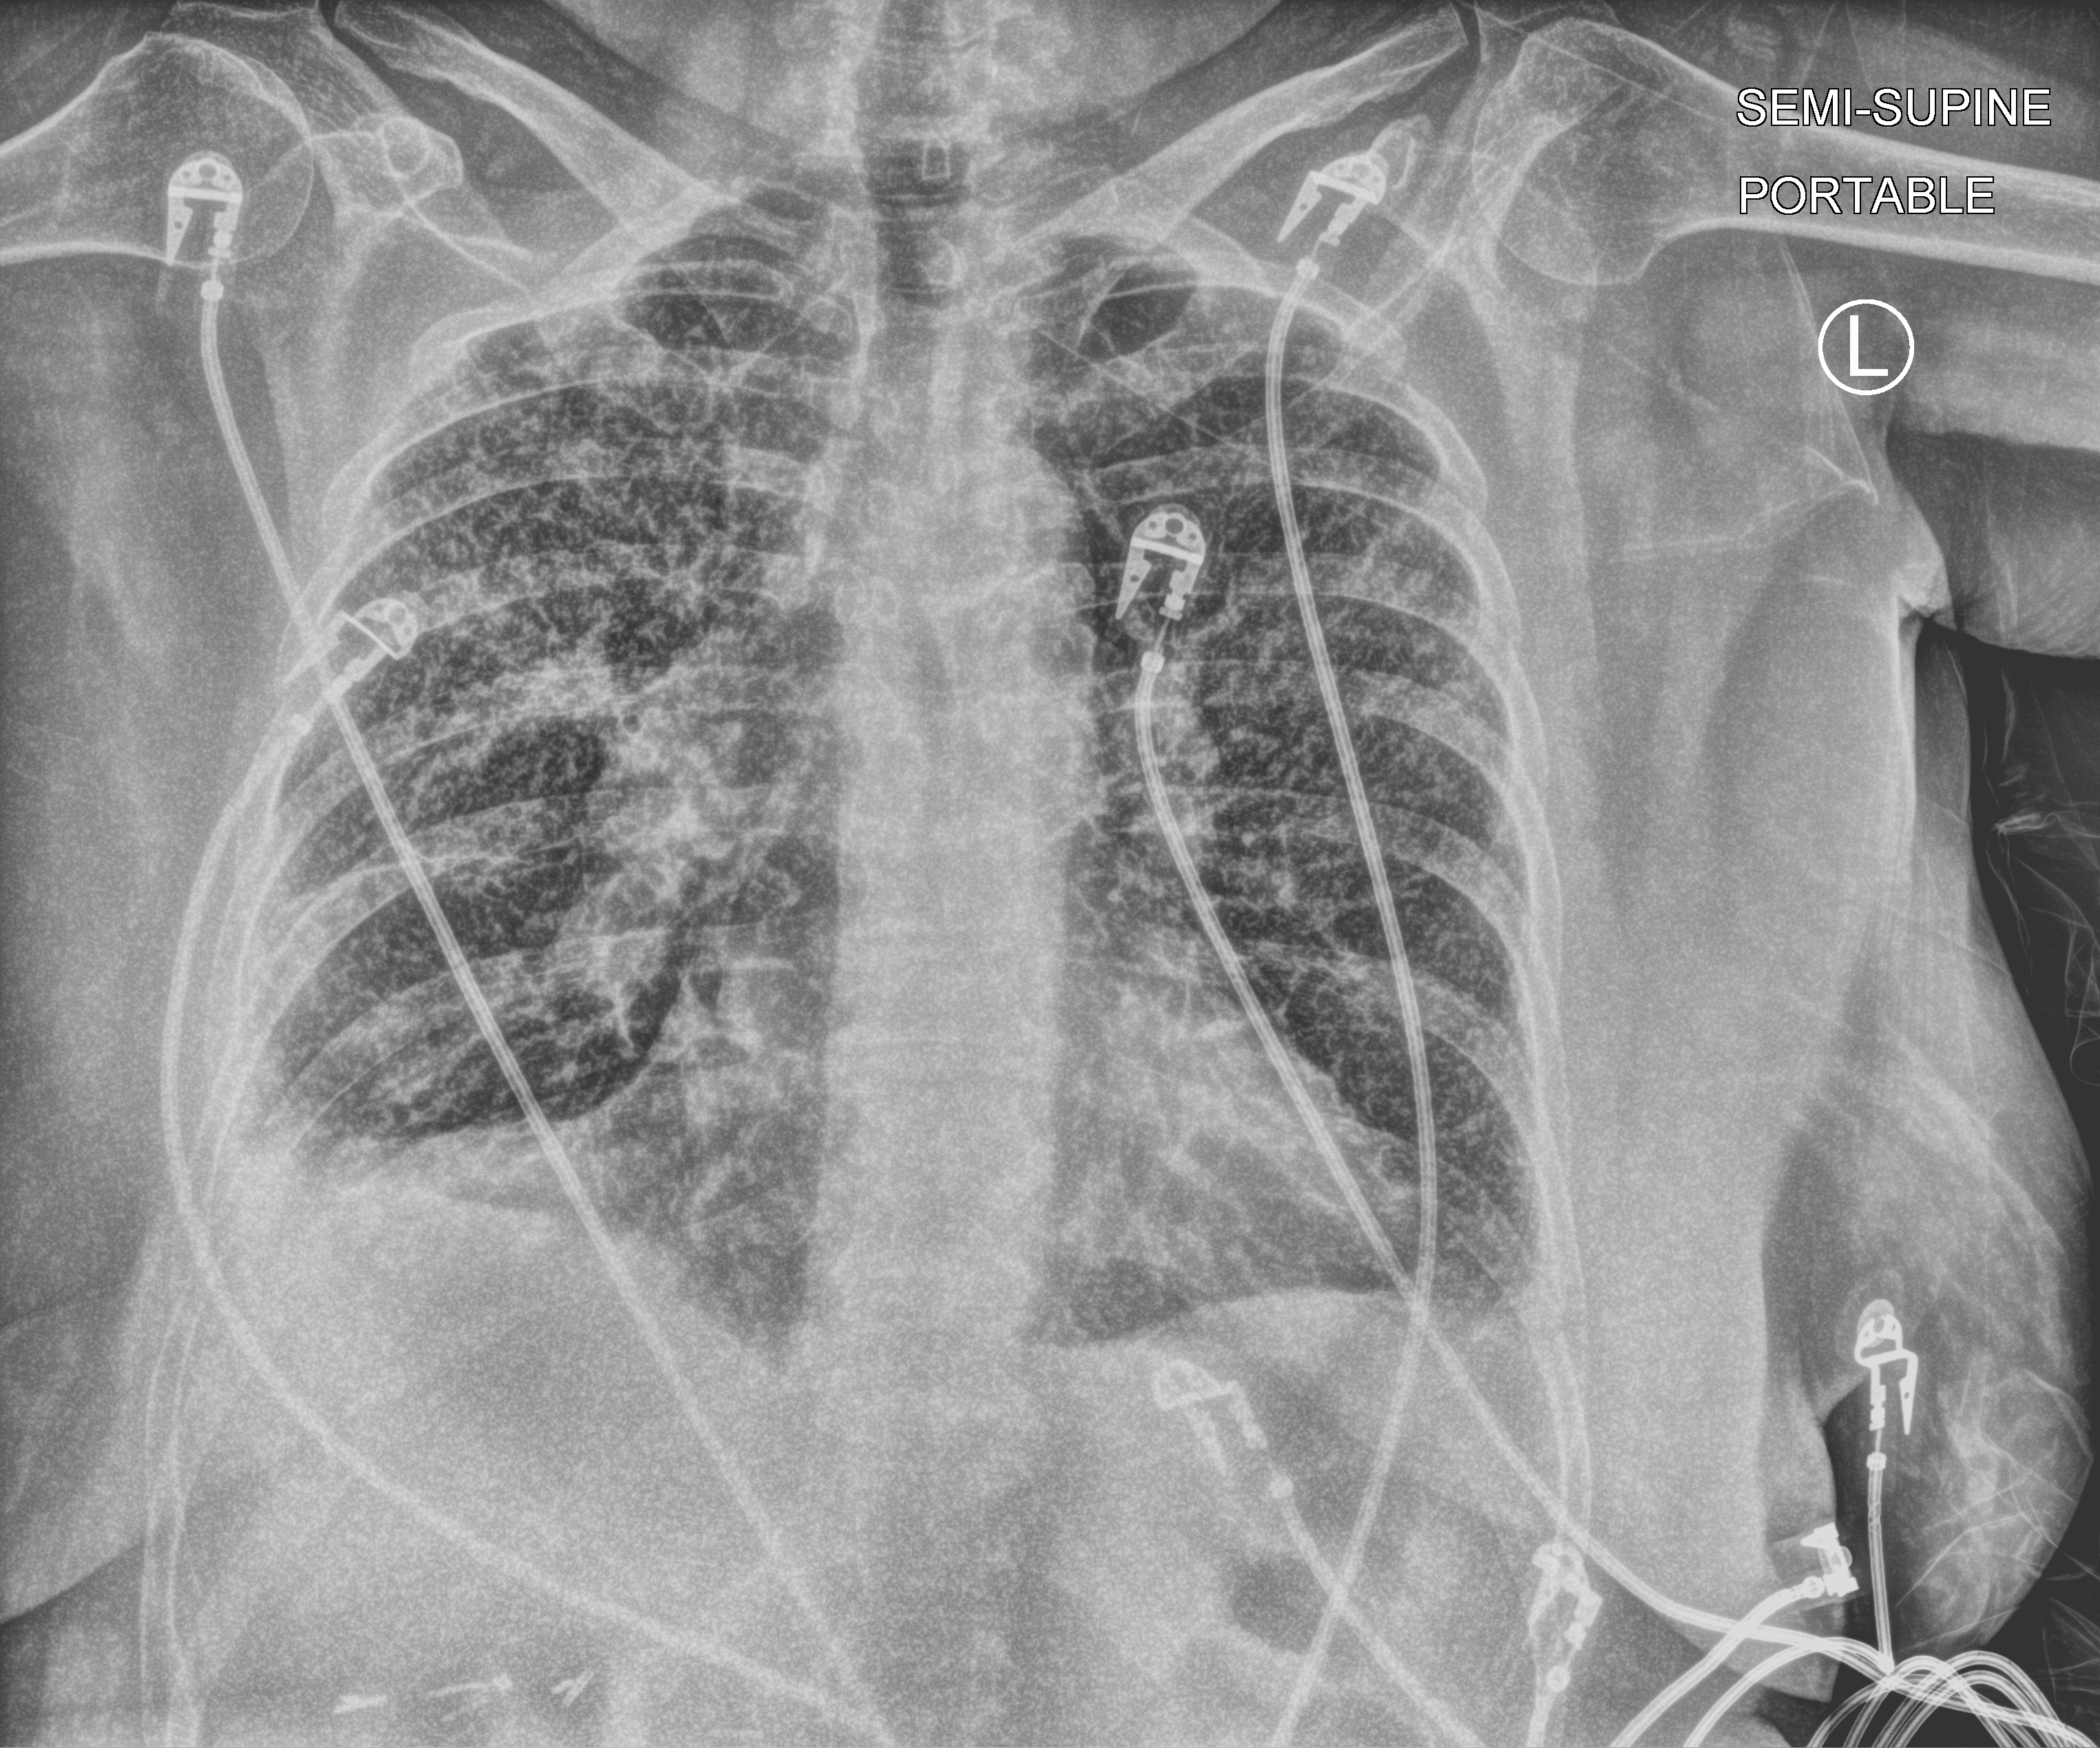
Chest X-ray (portable), anteroposterior (AP) projection. Patient hospitalised with COVID-19; female, aged 60–74 years.
Hospital-stay facts (about this admission, not read from this image; timing relative to this image not recorded):
- length of hospital stay: 19 days
- mechanically ventilated during this hospital stay: yes
- diabetes (admission record): no